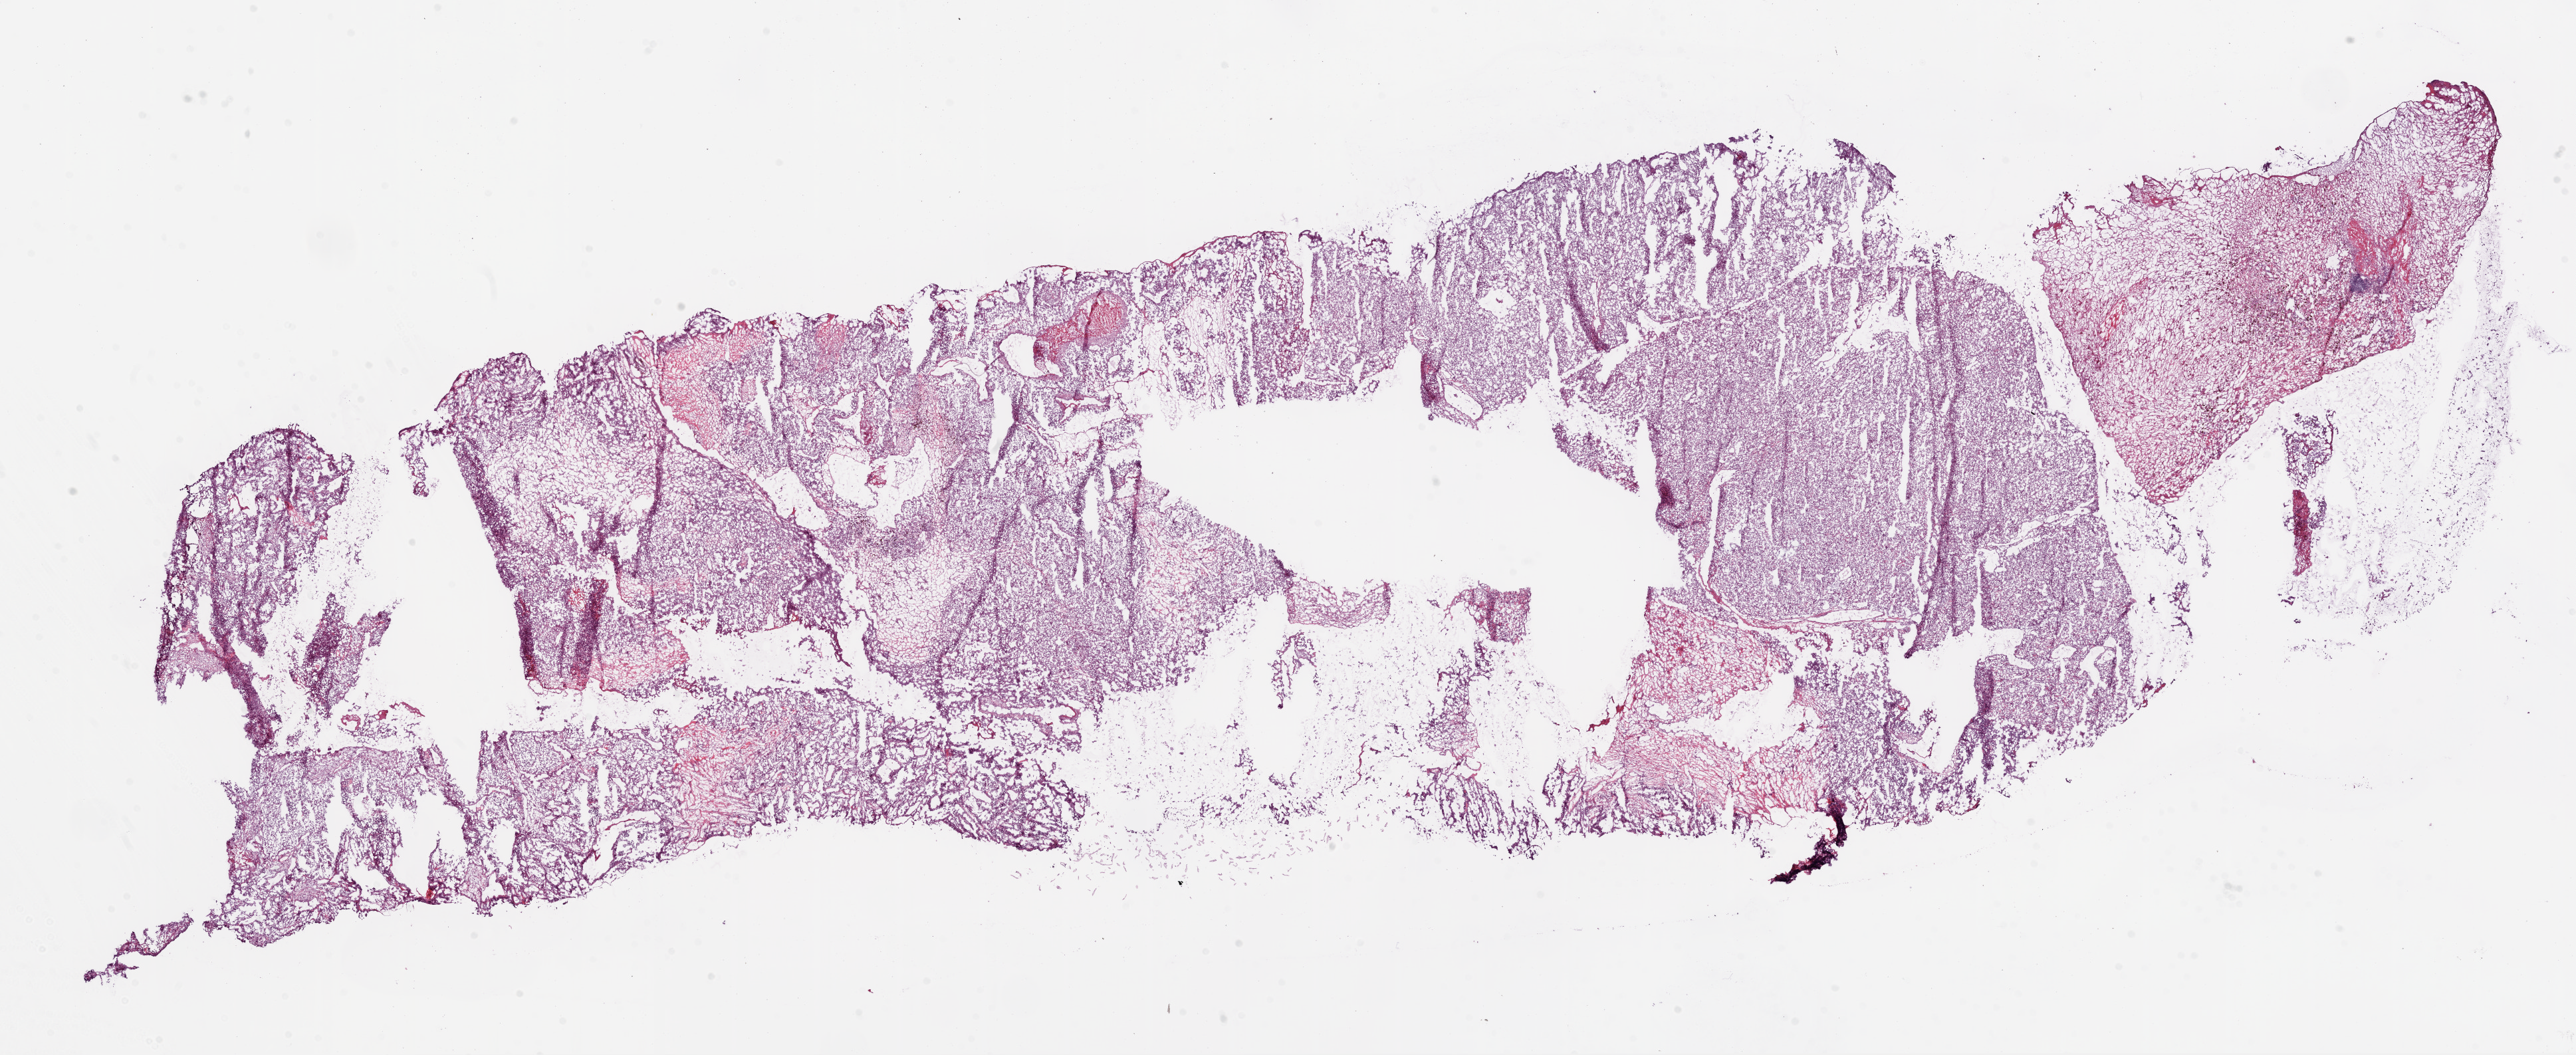
H&E whole-slide image — a low-resolution overview of the entire scanned area, about 31.1 x 12.7 mm; frozen section from the bottom of the tissue portion; primary tumour sample from the kidney. Male, age 62 years at initial diagnosis. Histologic grade: G4 (undifferentiated). Slide review estimates, as recorded: tumour cells 90%, tumour nuclei 85%, normal cells 0%, stromal cells 10%, necrosis 0%.
* laterality: left
* AJCC pathologic stage: IV
* diagnosis: Clear cell adenocarcinoma, NOS